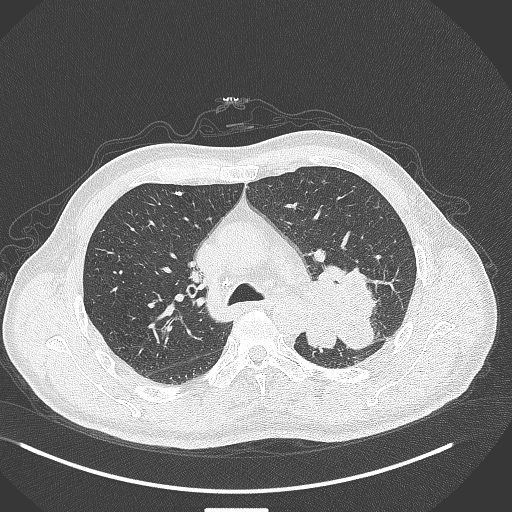
Chest CT, one axial slice. Position 283 of 429 along the scan axis. 120 kVp. Lung window (W 1500 / L -600 HU). 1 mm slice thickness. 512 × 512 image matrix. Patient: male, 55 years. Case-level facts recorded for this patient, not image findings: clinical TNM (as recorded): T3 N0 M1c.
Structures marked on this image (bounding box drawn by a radiologist):
- lung tumour (recorded histology: adenocarcinoma): bounding box <305,261,381,353> (left, top, right, bottom; pixels)